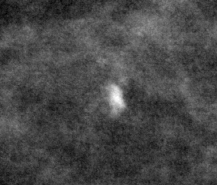
Region of interest cut from a scanned film mammogram (one marked finding), right breast, MLO view, BI-RADS breast density category 1 (scale 1–4).
Calcifications, morphology coarse; BI-RADS assessment category 2; benign without callback (not worked up further).